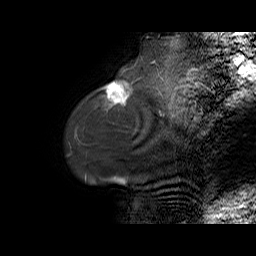
Breast MRI (dynamic contrast-enhanced), one sagittal slice. Position 11 of 70 along the scan axis. Dynamic contrast-enhanced series, time point 2 of 6 at this slice position (early post-contrast). 1.5 T. TE 5.5 ms, TR 32.9 ms. 4 mm slice thickness. 256 × 256 image matrix, field of view 240 × 240 mm. Female patient. Case-level facts recorded for this patient, not image findings: setting: breast cancer imaged before/during neoadjuvant chemotherapy; receptor status: HER2-positive.
Annotated regions visible in this slice (semi-automatic segmentation, software-assisted and operator-edited):
- analysis volume of interest (the breast-tissue region the enhancement analysis was run in; not a lesion): bounding box [x1, y1, x2, y2] px = [97, 81, 141, 106]
- tumour enhancement mask (voxels above the 100 % enhancement threshold inside the analysis volume of interest): [107, 82, 130, 104]